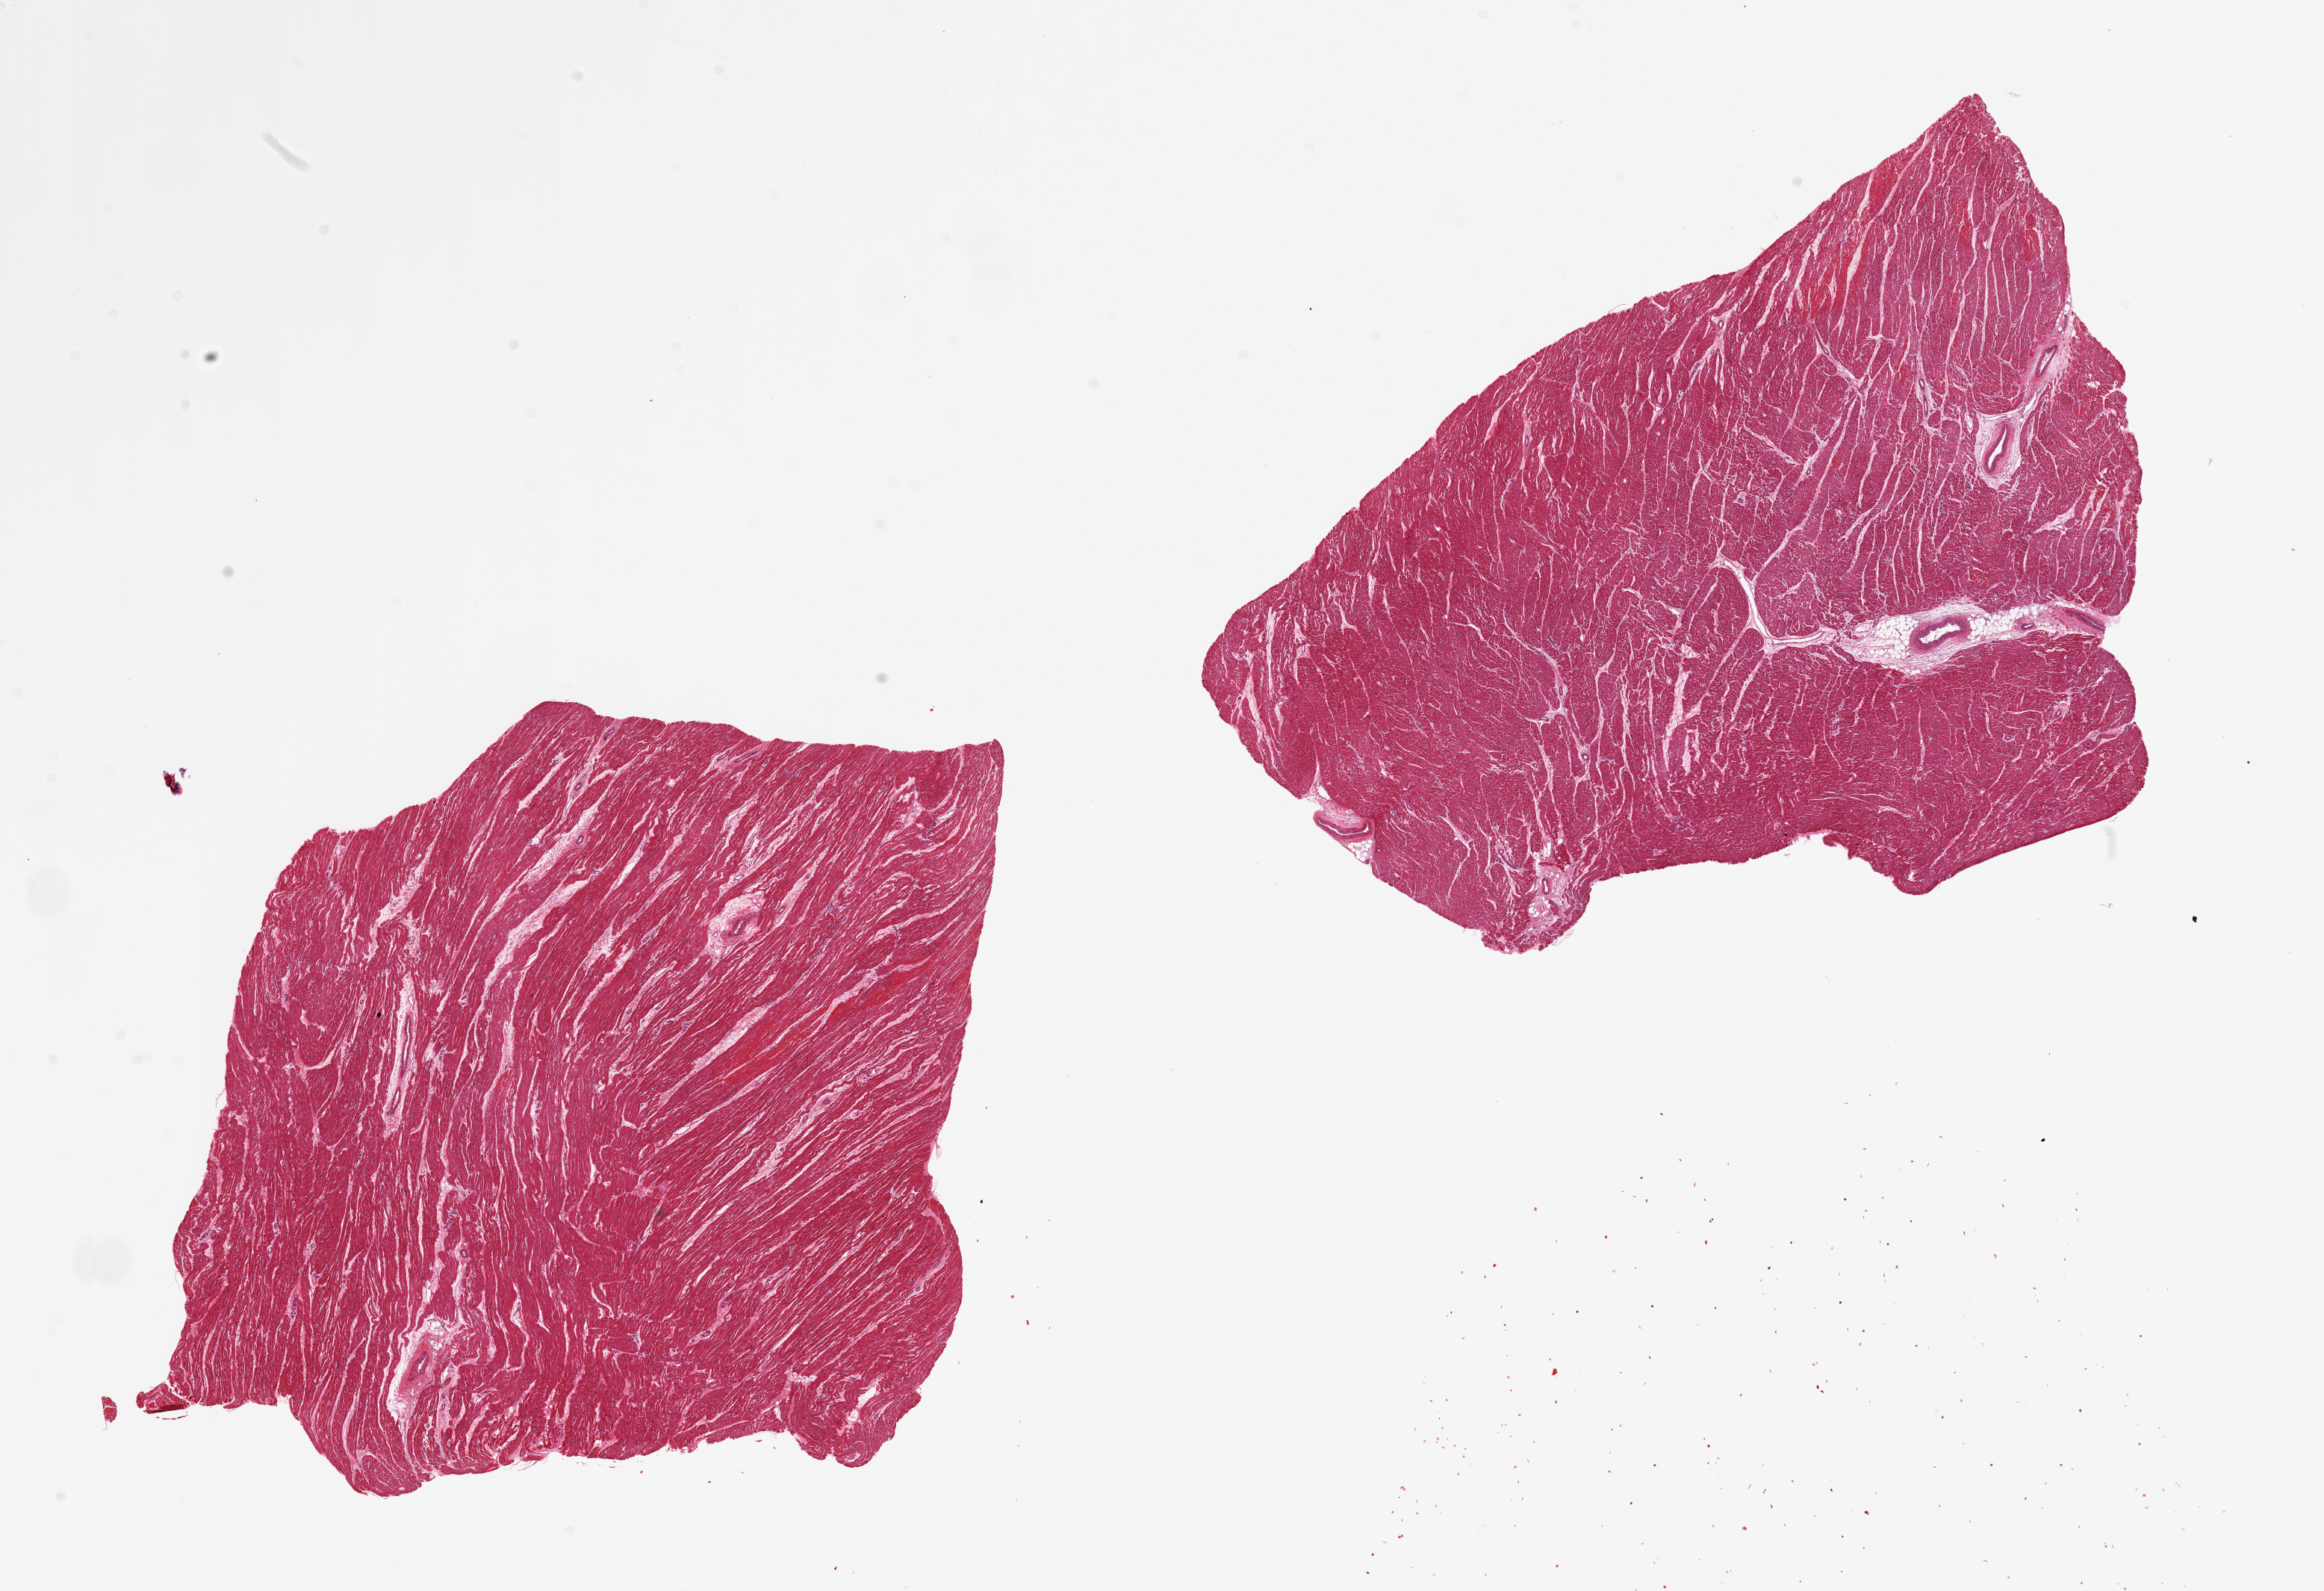
Hematoxylin and eosin (H&E) whole-slide image — whole scanned area (about 24.6 x 16.8 mm, acquisition: 20x scan) shown as a low-resolution overview. PAXgene-fixed paraffin-embedded (PFPE) section. Section of heart (target tissue). Donor tissue sample. Female donor.
* pathologist's review note for this sample: 2 pieces, diffuse myocarditis, mild-moderate, focal myocyte damage noted; findings may reflect history of recent cardicac transplant 3 d prior to demise (ie rejection vs reactive inflammation)